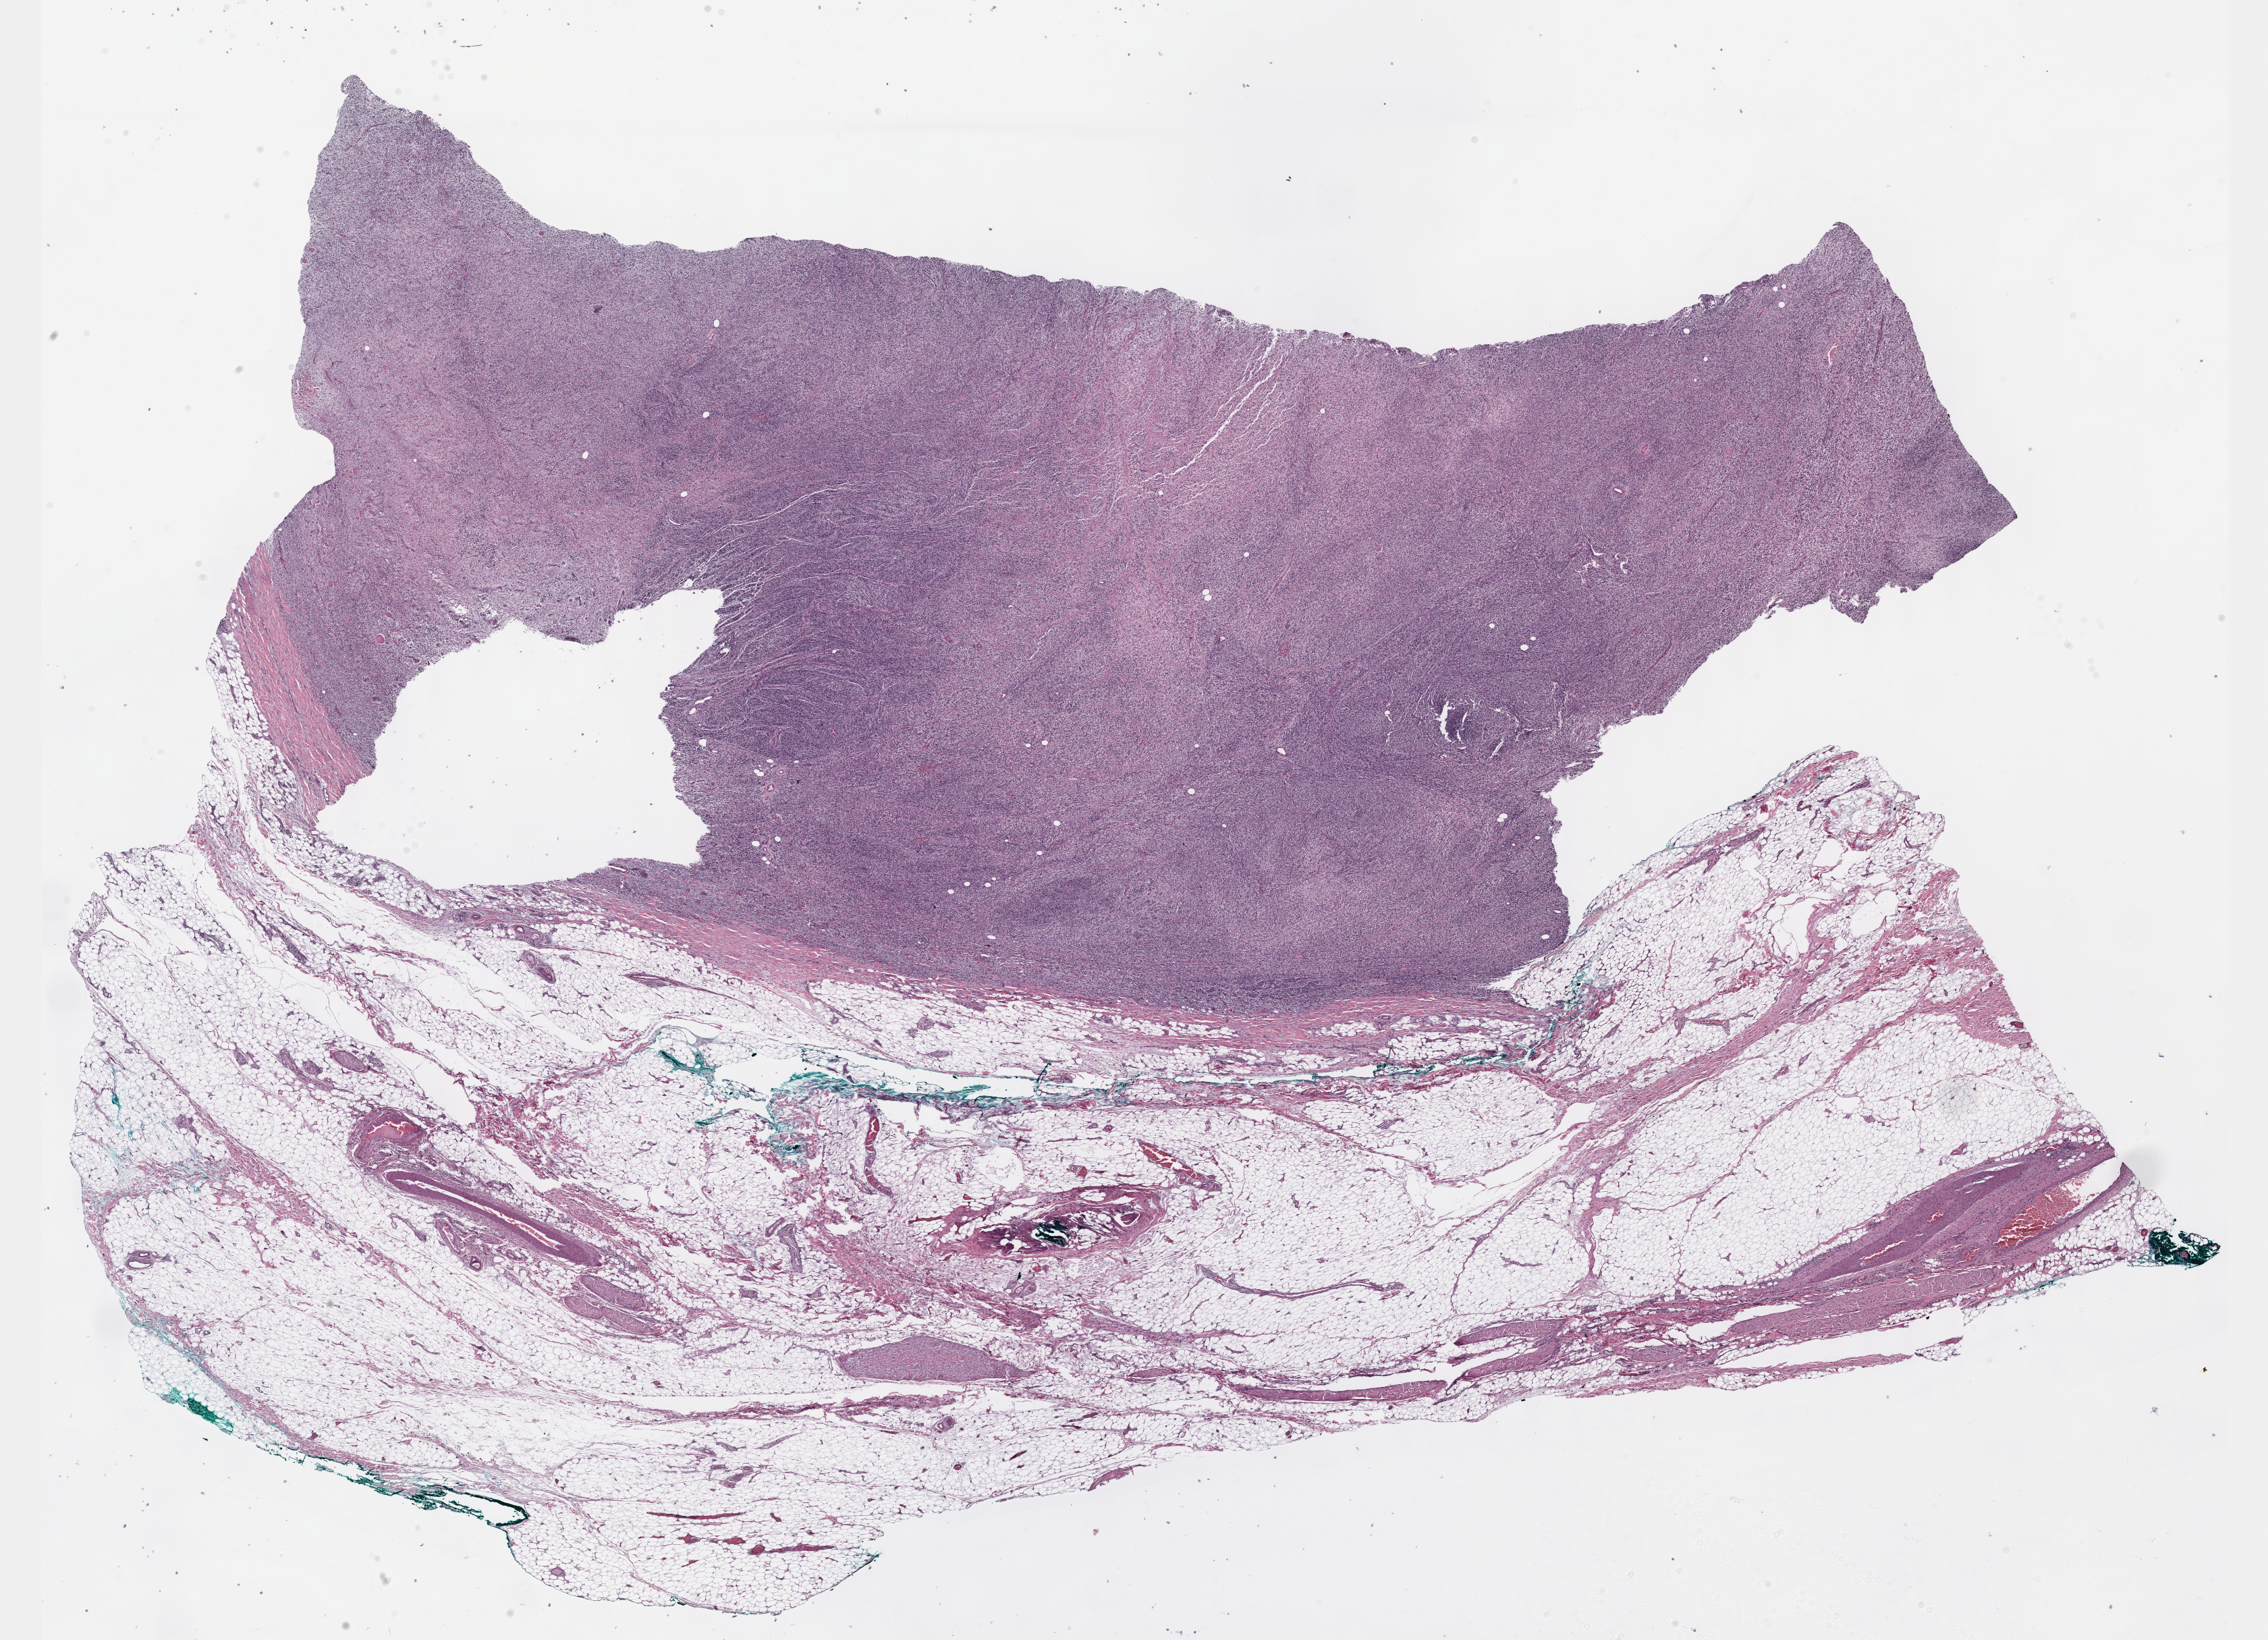
Hematoxylin and eosin (H&E) stained whole-slide image, shown as a low-resolution overview of the whole scanned area (about 27.2 x 19.6 mm), formalin-fixed paraffin-embedded (FFPE) diagnostic section, connective, subcutaneous and other soft tissues, primary tumour sample. Female patient; age at initial diagnosis 34 years.
Histologic diagnosis: Malignant peripheral nerve sheath tumor.